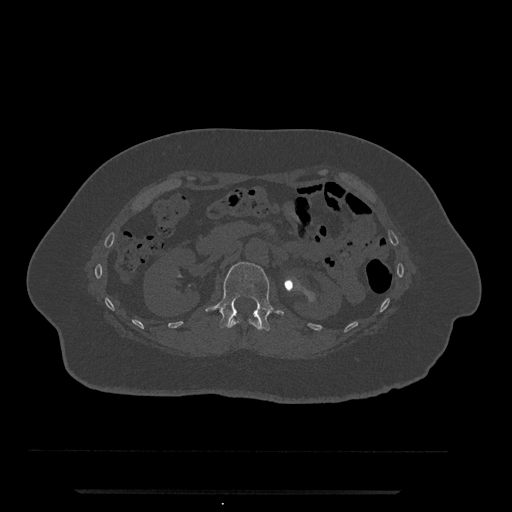
CT including the spine, one axial slice; position 118 of 797 along the scan axis; 120 kVp; bone window (W 1800 / L 400 HU); 0.5 mm slice thickness; 512 × 512 image matrix, field of view 440 × 440 mm. Female patient, age 51 years. Case-level facts recorded for this patient, not image findings: primary cancer: neuro.
Structures marked on this image (semi-automatically segmented with operator editing):
- L1 vertebra: box from (x=206, y=262) to (x=284, y=331) px
- T12 vertebra: (x=229, y=318)–(x=262, y=331)